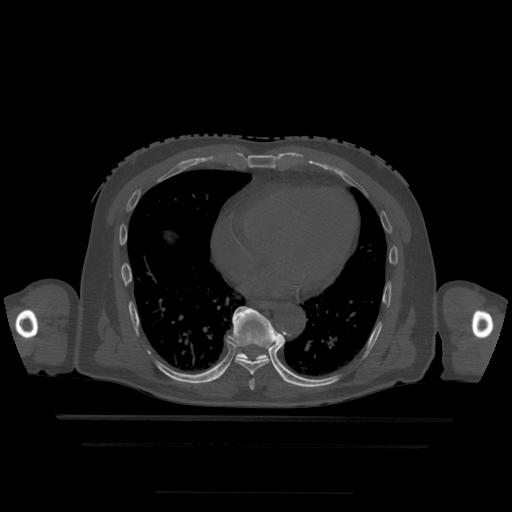
CT including the spine, one axial slice; slice 275 of 522 in the series (ordered by position); bone window (W 1800 / L 400 HU); 1.25 mm slice thickness; 512 × 512 image matrix. Patient age 68 years. From the clinical record (not read from this slice): primary cancer: urothelial.
Outlined on this slice (semi-automatically segmented with operator editing):
- T7 vertebra: bounding box (x1, y1, x2, y2) in pixels: (249, 380, 255, 390)
- T8 vertebra: (232, 307, 279, 376)
- T9 vertebra: (233, 313, 268, 361)